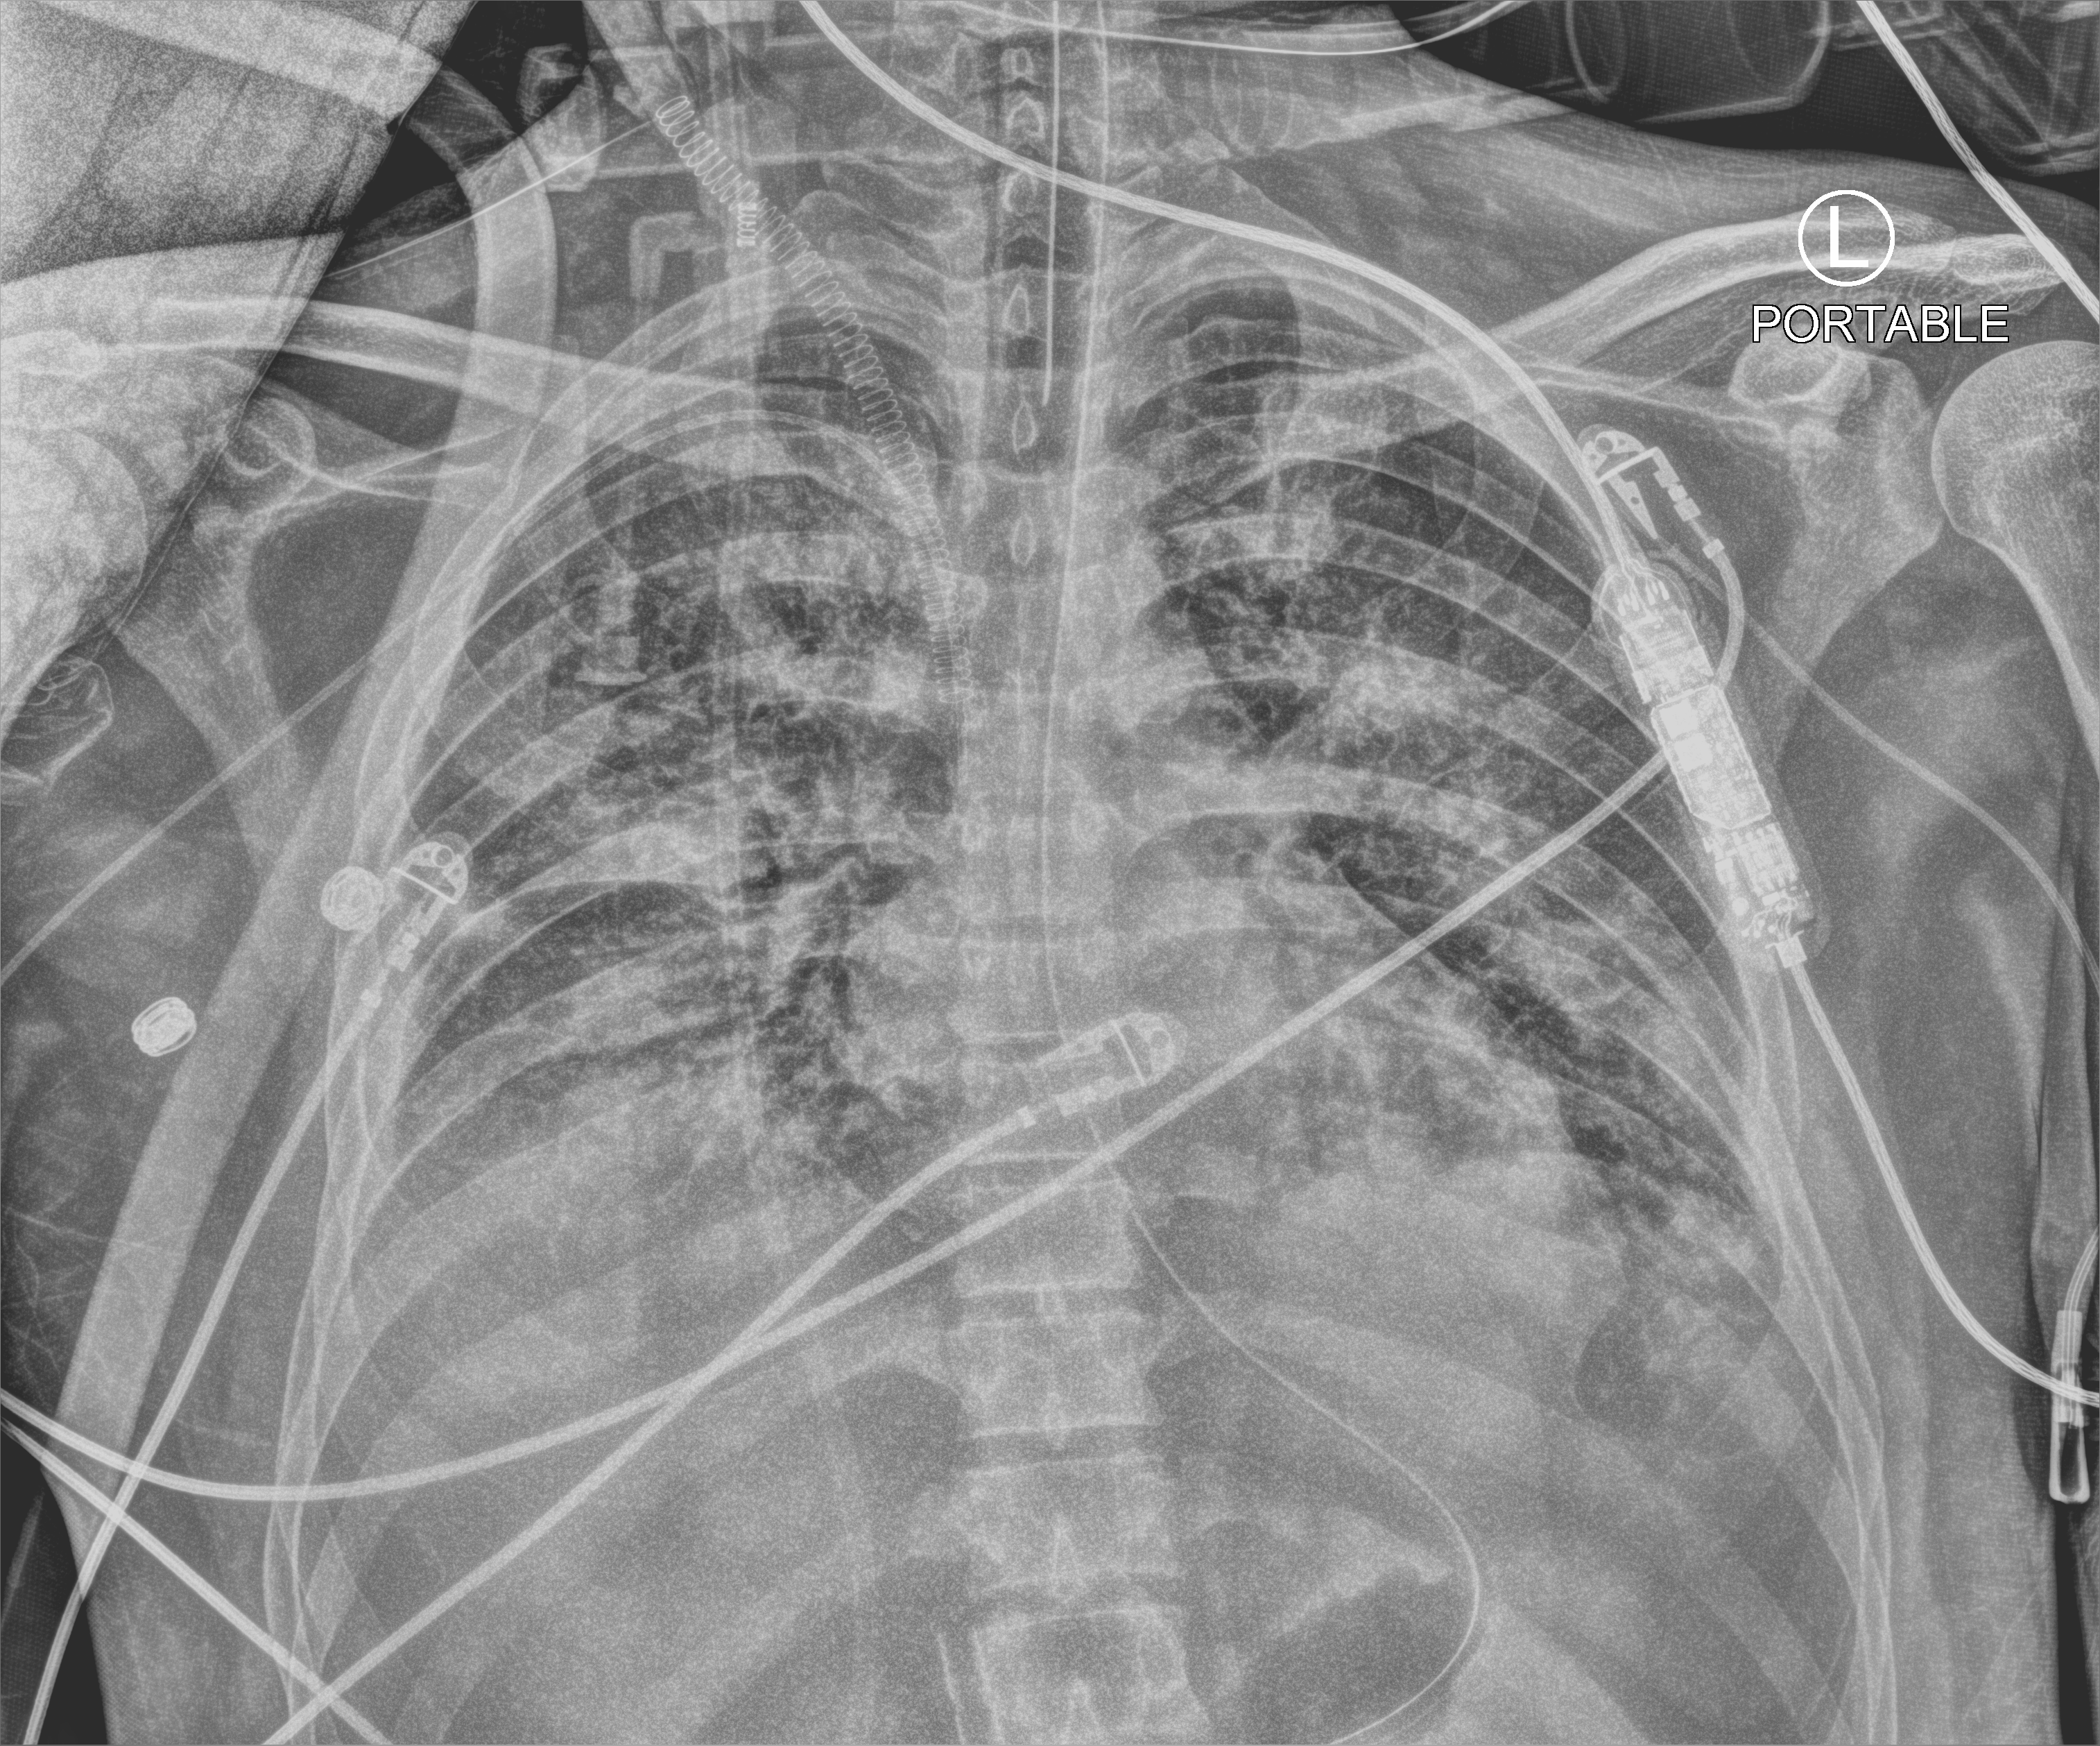
Chest X-ray (portable), anteroposterior (AP) projection. Patient hospitalised with COVID-19, aged 18–59 years.
Admission-level facts for this patient (not findings on this image; timing relative to this image not recorded):
- admitted to intensive care during this hospital stay: yes
- mechanically ventilated during this hospital stay: yes